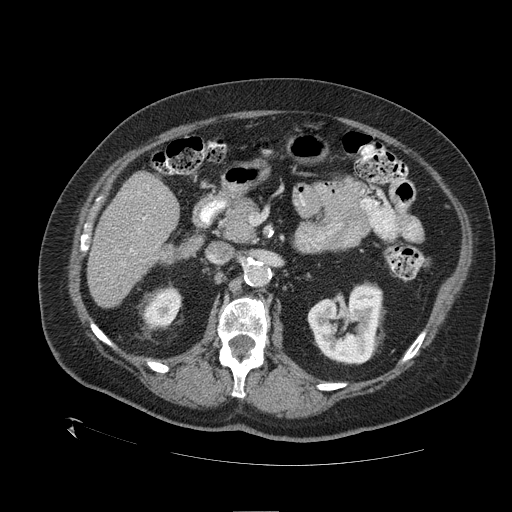
Contrast-enhanced abdominal CT (liver protocol), one axial slice; reconstruction kernel STANDARD; one of 2 acquisitions stored at this slice position; soft-tissue window (W 400 / L 40 HU); 2.5 mm slice thickness; 512 × 512 image matrix, field of view 460 × 460 mm. Case-level facts recorded for this patient, not image findings: diagnosis: hepatocellular carcinoma (patient treated with transarterial chemoembolisation; whether this scan precedes or follows treatment is not stated here); TNM stage (as recorded): Stage-I; Child-Pugh class: A; tumour differentiation: no biopsy; tumour nodularity: uninodular.
Outlined on this slice (semi-automatically segmented with operator editing):
- liver parenchyma outside the tumour (the mass and vessels are separate outlines, so this box may not span the whole liver): box from (x=88, y=172) to (x=178, y=308) px
- liver vessels: (x=130, y=217)–(x=146, y=252)